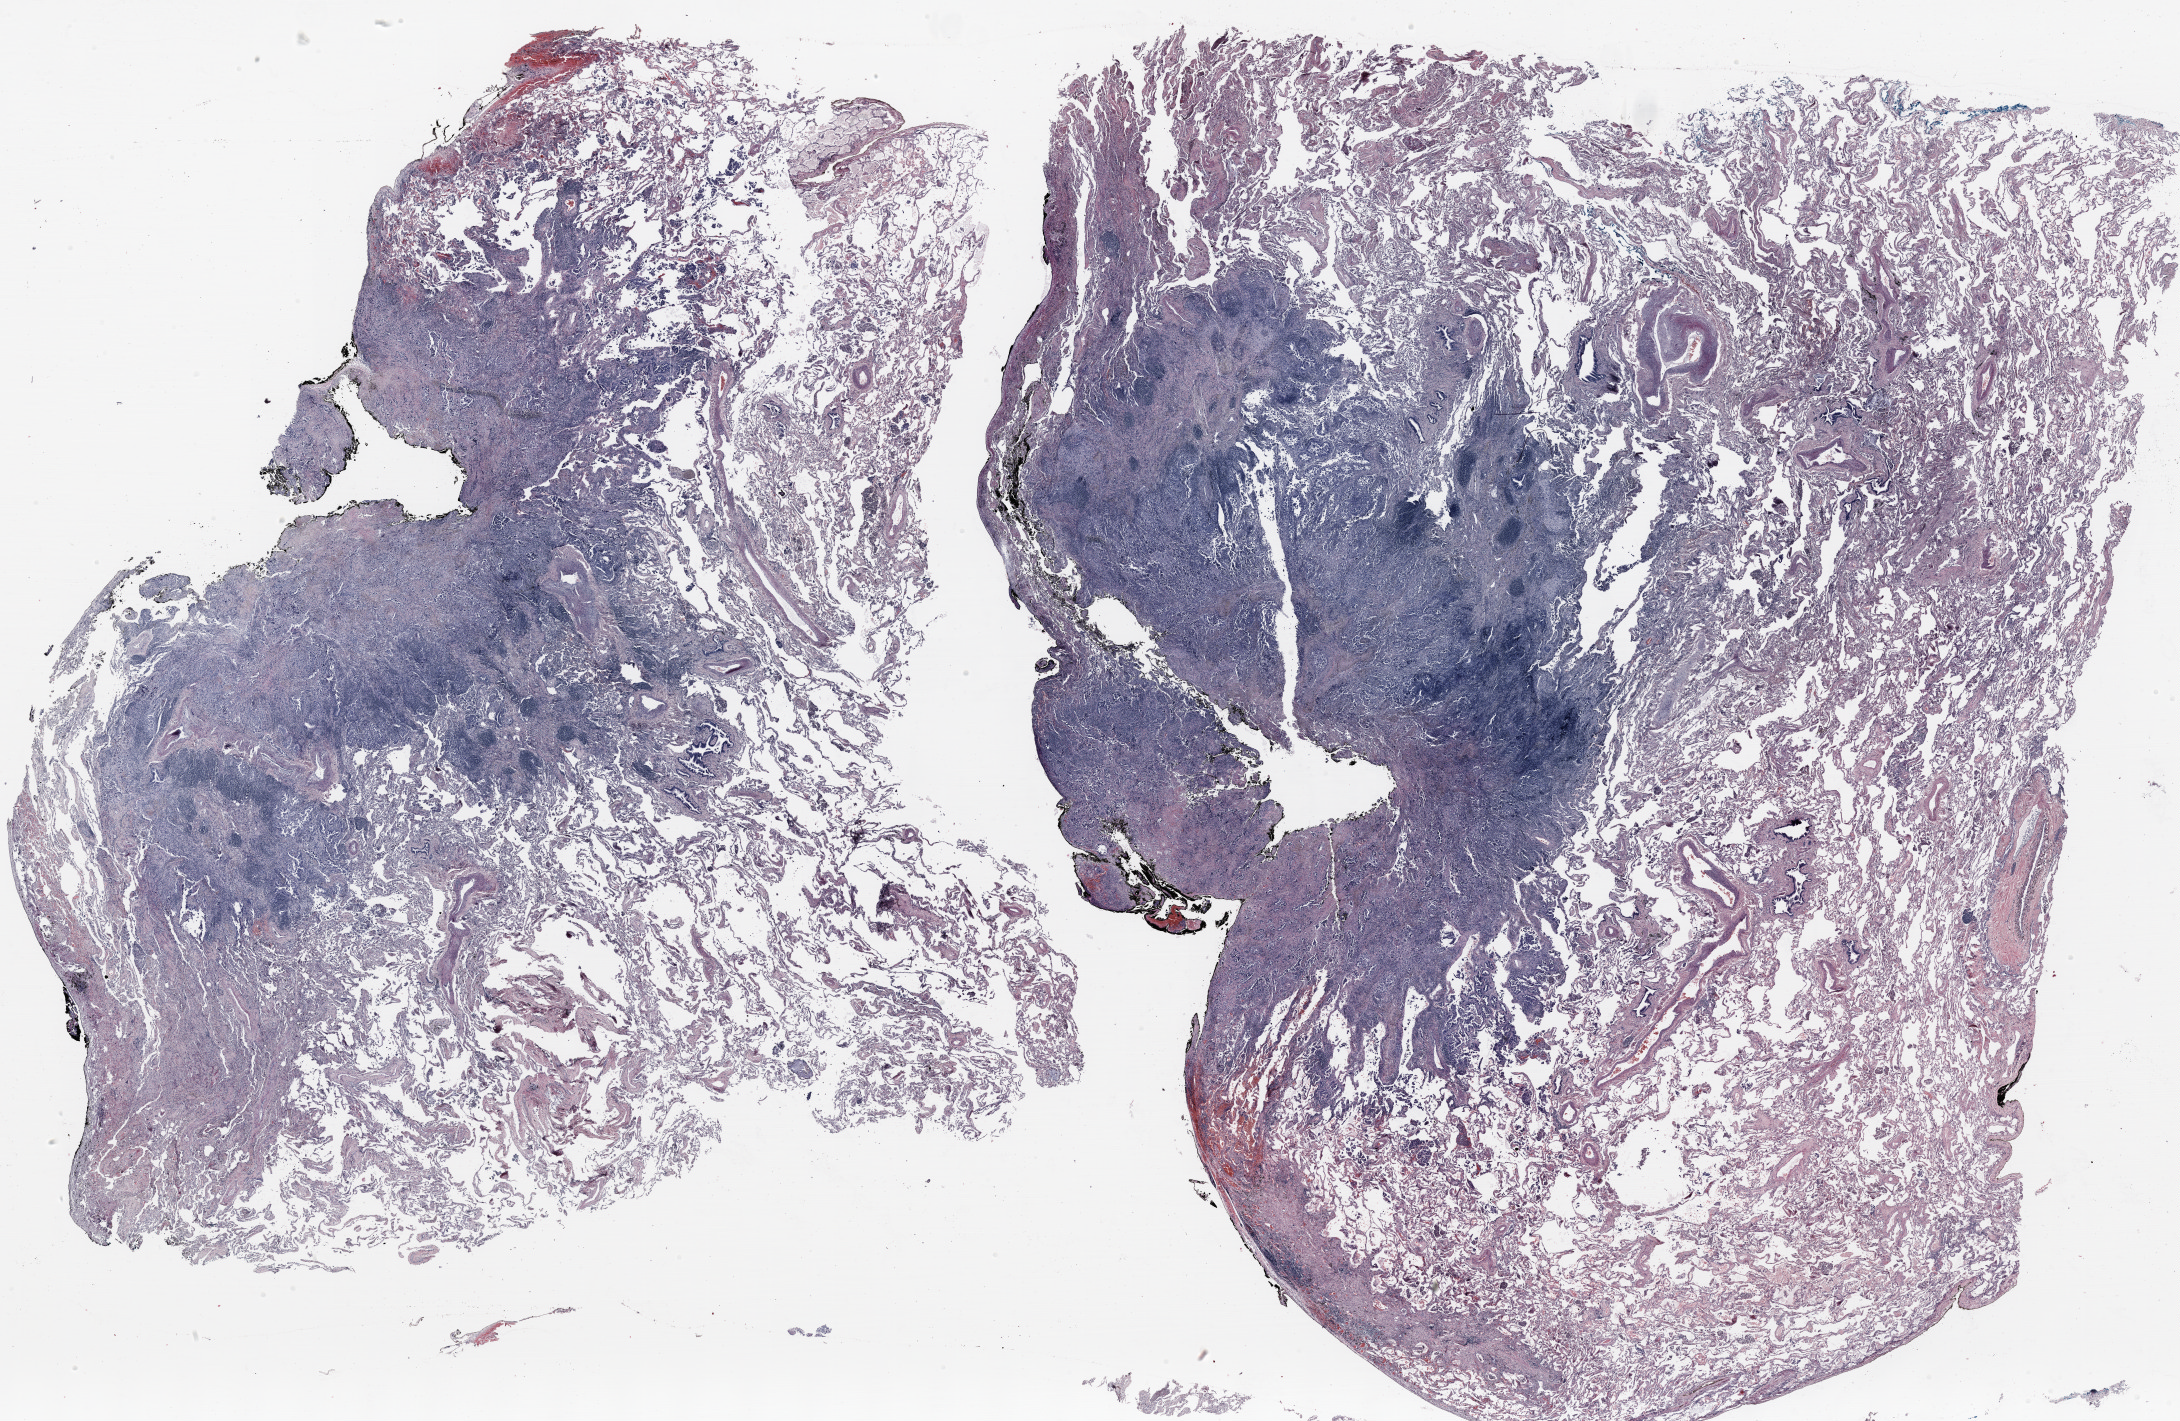
H&E-stained whole-slide image — whole scanned area (about 35.0 x 22.8 mm, slide scanned at 20x) shown as a low-resolution overview, FFPE section, lung. Female patient, aged 66 at enrolment. Current smoker at enrolment. Grade: moderately differentiated (G2).
• participant's lung-cancer diagnosis: Adenocarcinoma, NOS
• ICD-O-3 topography: upper lobe of lung (C34.1)
• tumour size (pathology): 17 mm
• stage (AJCC 6th edition): IB
• primary tumour location (clinical record): left upper lobe
• note: participant had 2 primary lung cancers recorded; fields above describe the first